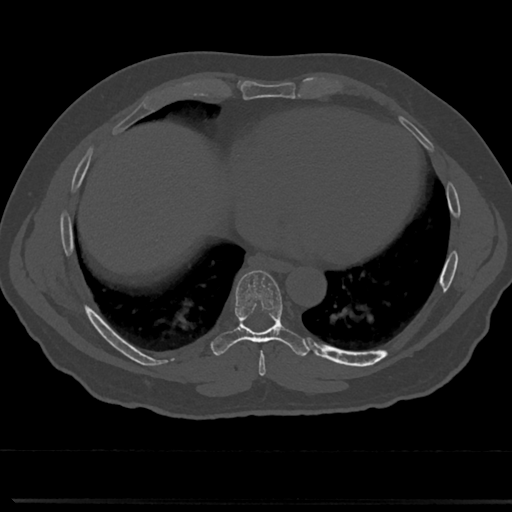
CT including the spine, one axial slice; slice 360 of 817 in the series (ordered by position); reconstruction kernel Br40s/3; 120 kVp; bone window (W 1800 / L 400 HU); 512 × 512 image matrix, field of view 355 × 355 mm. Patient: male, 61 years. From the clinical record (not read from this slice): primary cancer: prostate.
Structures marked on this image (semi-automatic segmentation, software-assisted and operator-edited):
- T7 vertebra: bounding box <238,309,285,361> (left, top, right, bottom; pixels)
- T8 vertebra: <237,271,283,336>